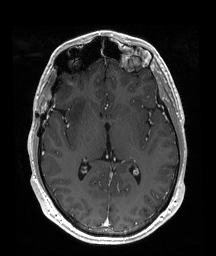
Brain MRI from a brain-tumour surgery series, one axial slice; position 104 of 192 along the scan axis; T1-weighted post-contrast; 216 × 256 image matrix. Case-level facts recorded for this patient, not image findings: histopathology: Astrocytoma; WHO grade: 2; IDH mutation: yes; tumour location: Right Insular.
Outlined on this slice (manually delineated by an expert):
- tumour: bounding box [x1, y1, x2, y2] px = [68, 94, 91, 130]